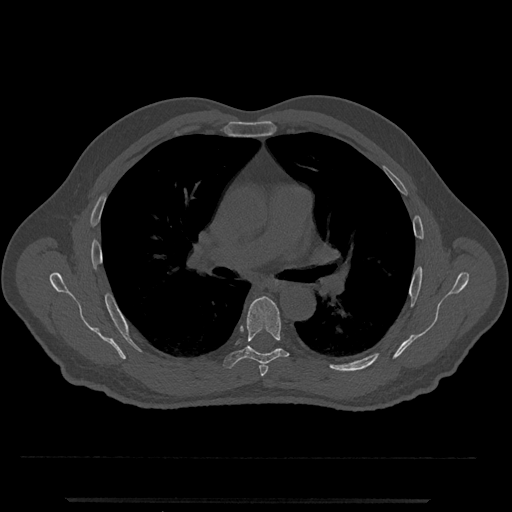
CT including the spine, one axial slice. Position 743 of 797 along the scan axis. Reconstruction kernel Br40s/3. 120 kVp. Bone window (W 1800 / L 400 HU). 0.5 mm slice thickness. 512 × 512 image matrix, field of view 419 × 419 mm. Male patient, age 63 years. Case-level facts recorded for this patient, not image findings: primary cancer: prostate.
Annotated regions visible in this slice (semi-automatically segmented with operator editing):
- T5 vertebra: bounding box (x1, y1, x2, y2) in pixels: (259, 363, 268, 377)
- T6 vertebra: (223, 296, 289, 368)